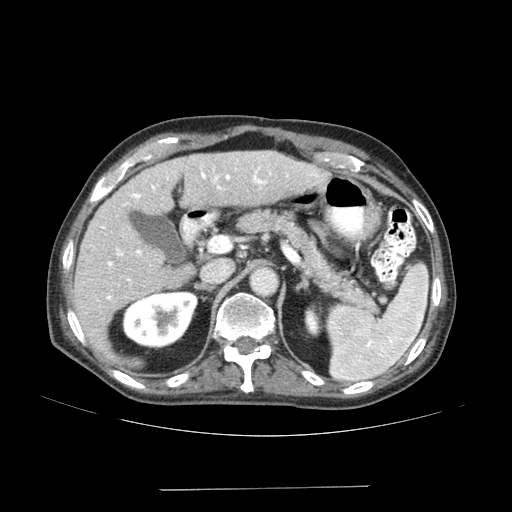
Contrast-enhanced abdominal CT (liver protocol), one axial slice; position 96 of 192 along the scan axis; soft-tissue window (W 400 / L 40 HU); 2.5 mm slice thickness; 512 × 512 image matrix, field of view 400 × 400 mm. From the clinical record (not read from this slice): diagnosis: hepatocellular carcinoma (patient treated with transarterial chemoembolisation; whether this scan precedes or follows treatment is not stated here); TNM stage (as recorded): Stage-IVA; Child-Pugh class: A; tumour differentiation: poorly differentiated; tumour nodularity: uninodular.
Structures marked on this image (semi-automatically segmented with operator editing):
- liver parenchyma outside the tumour (the mass and vessels are separate outlines, so this box may not span the whole liver): bounding box (x1, y1, x2, y2) in pixels: (72, 150, 328, 350)
- liver vessels: (102, 167, 318, 300)